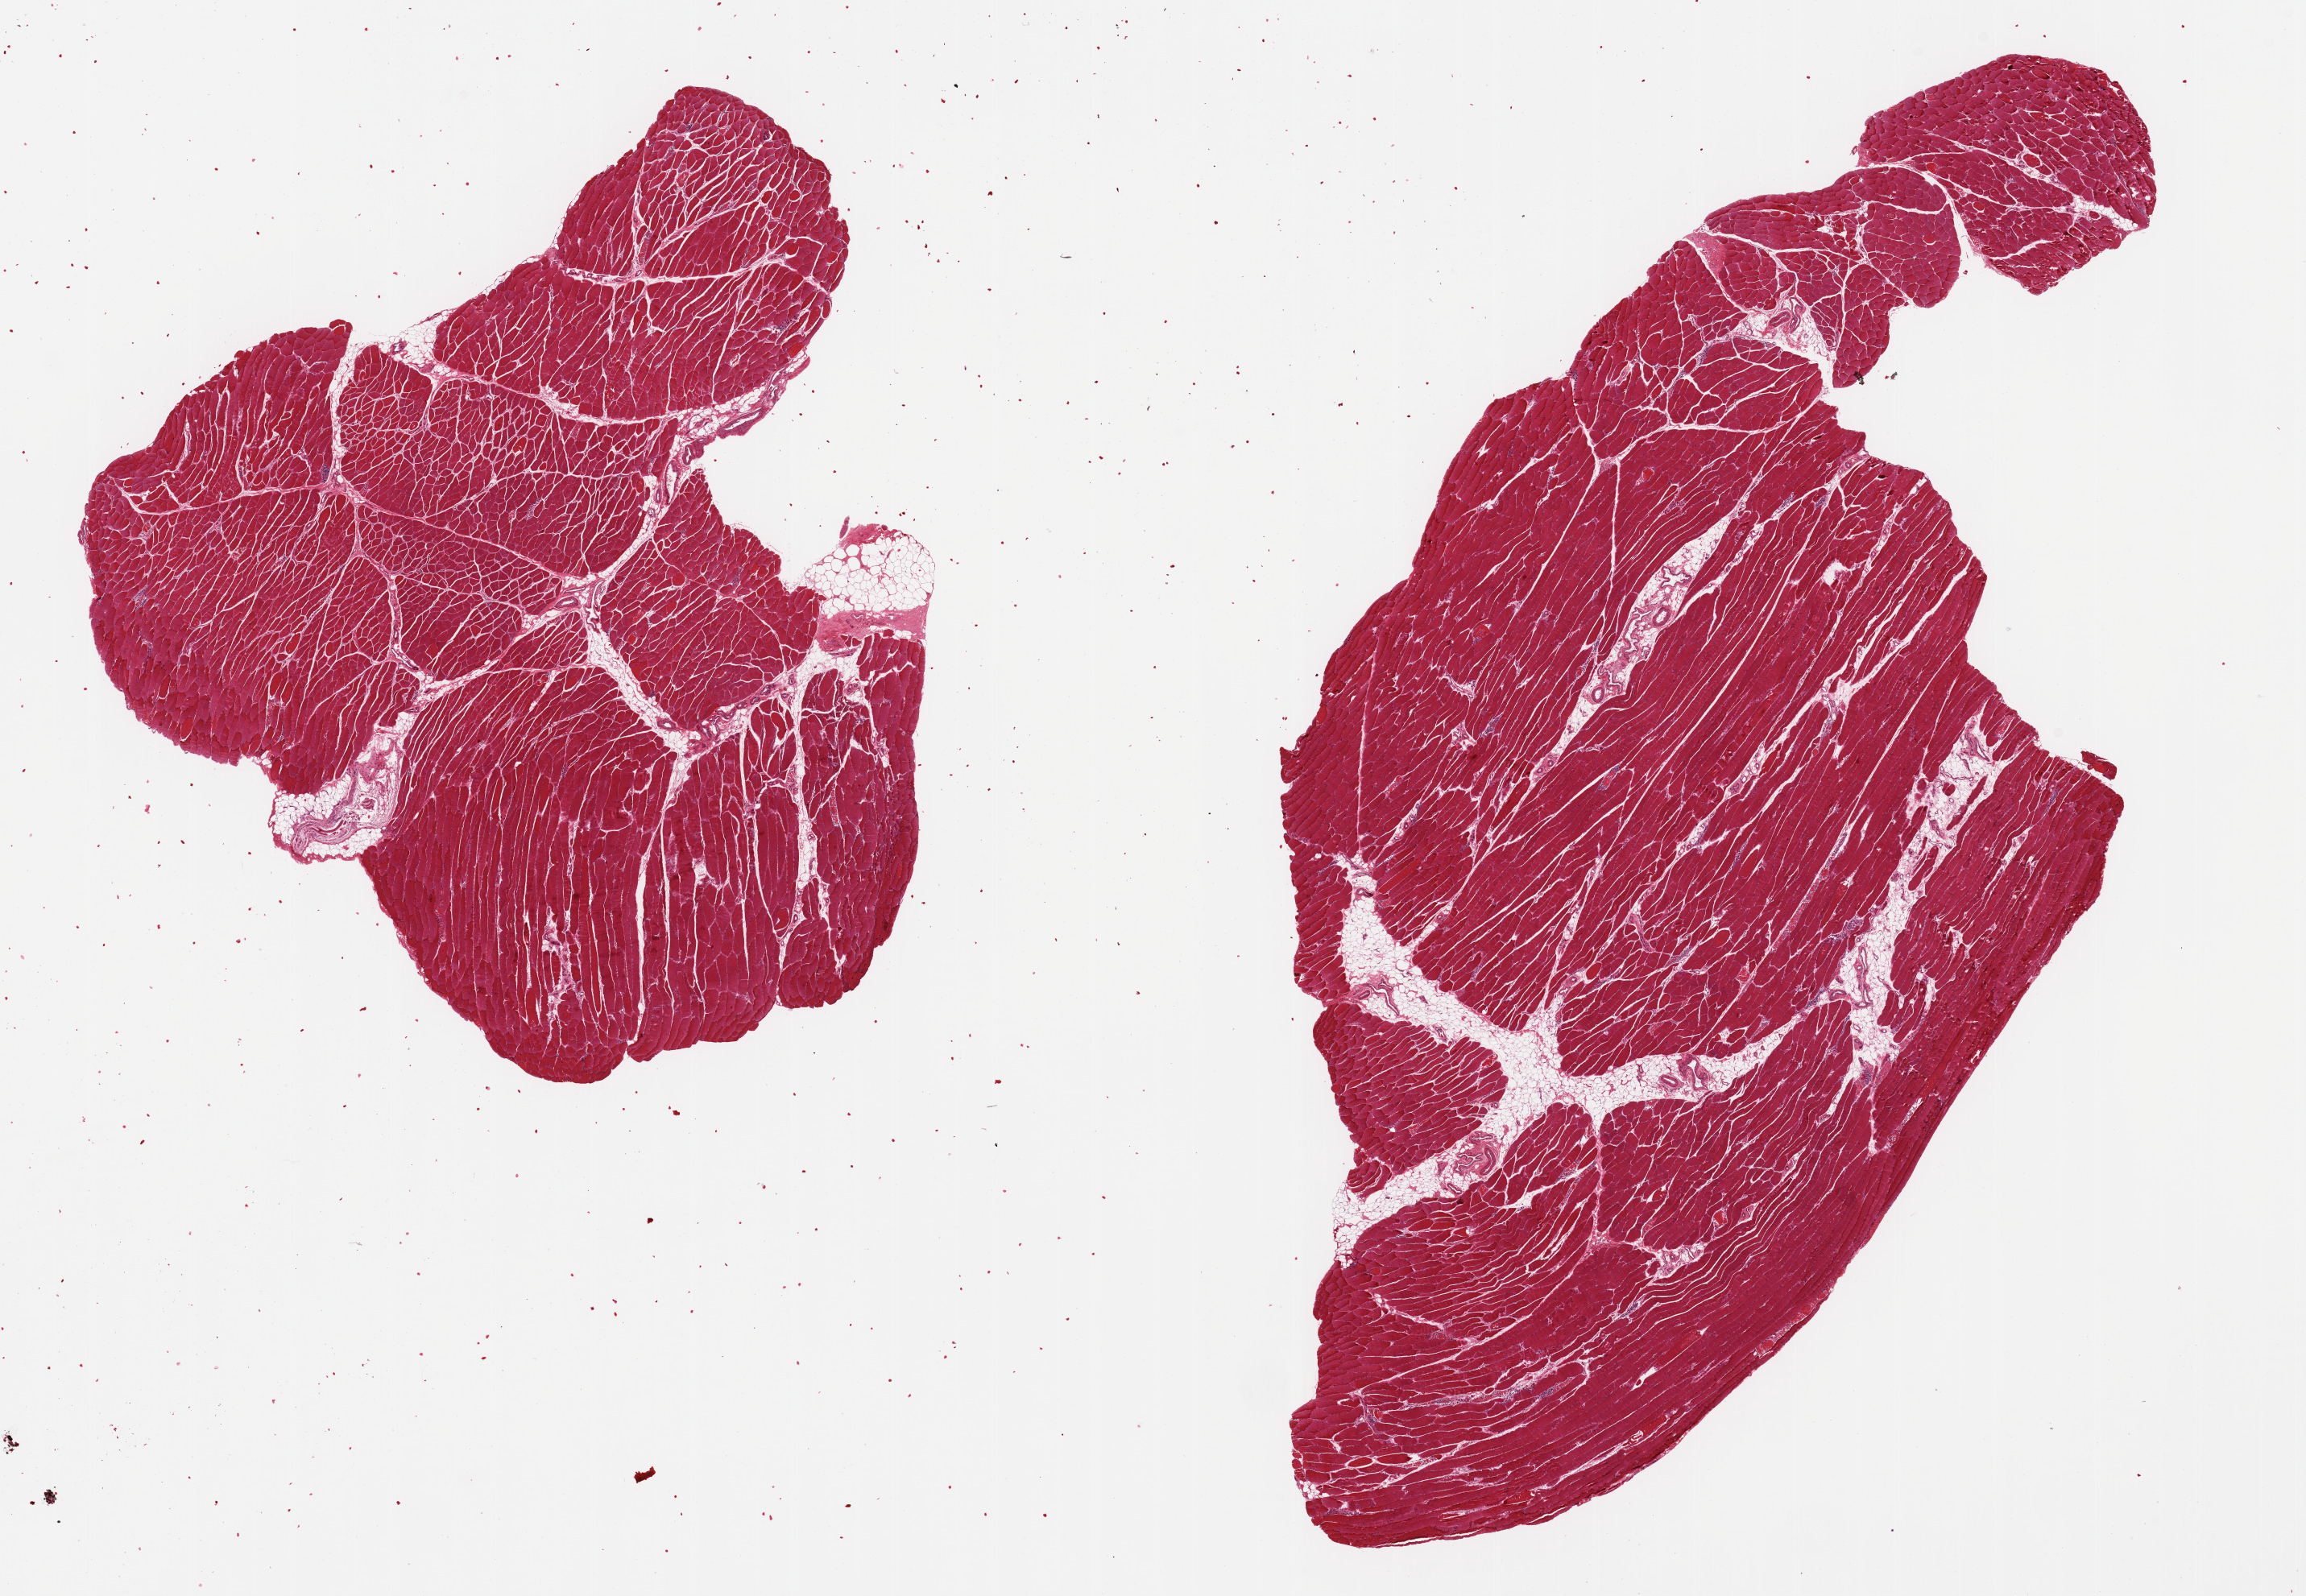
H&E whole-slide image — whole scanned area (about 22.6 x 15.7 mm, slide scanned at 20x) shown as a low-resolution overview, PAXgene-fixed paraffin-embedded (PFPE) section, target tissue: skeletal muscle, donor tissue sample. Donor: male.
Reviewer comment on this tissue sample: 2 pieces; includes 5-10% mostly internal fat.